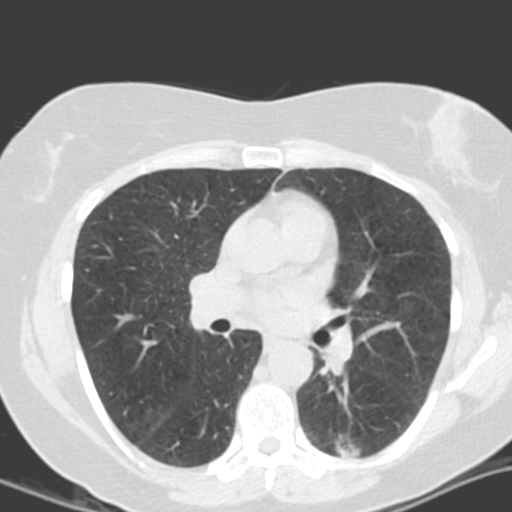
Axial slice from a low-dose chest CT screening exam. Second screening round (one year after baseline). Lung window (W 1500 / L -600 HU). 3.2 mm slice thickness. Slice 65 of 161 in the series. 512 × 512 image matrix, field of view 290 × 290 mm. Female, age 55 years at enrolment.
Lesion marked by an expert reader, bounding box (x1, y1, x2, y2) in pixels: (304, 410, 380, 472). The screening reader recorded 4 non-calcified nodules or masses ≥4 mm on this exam (left lower lobe, left lower lobe, left upper lobe, right middle lobe); which of them this box marks is not recorded.